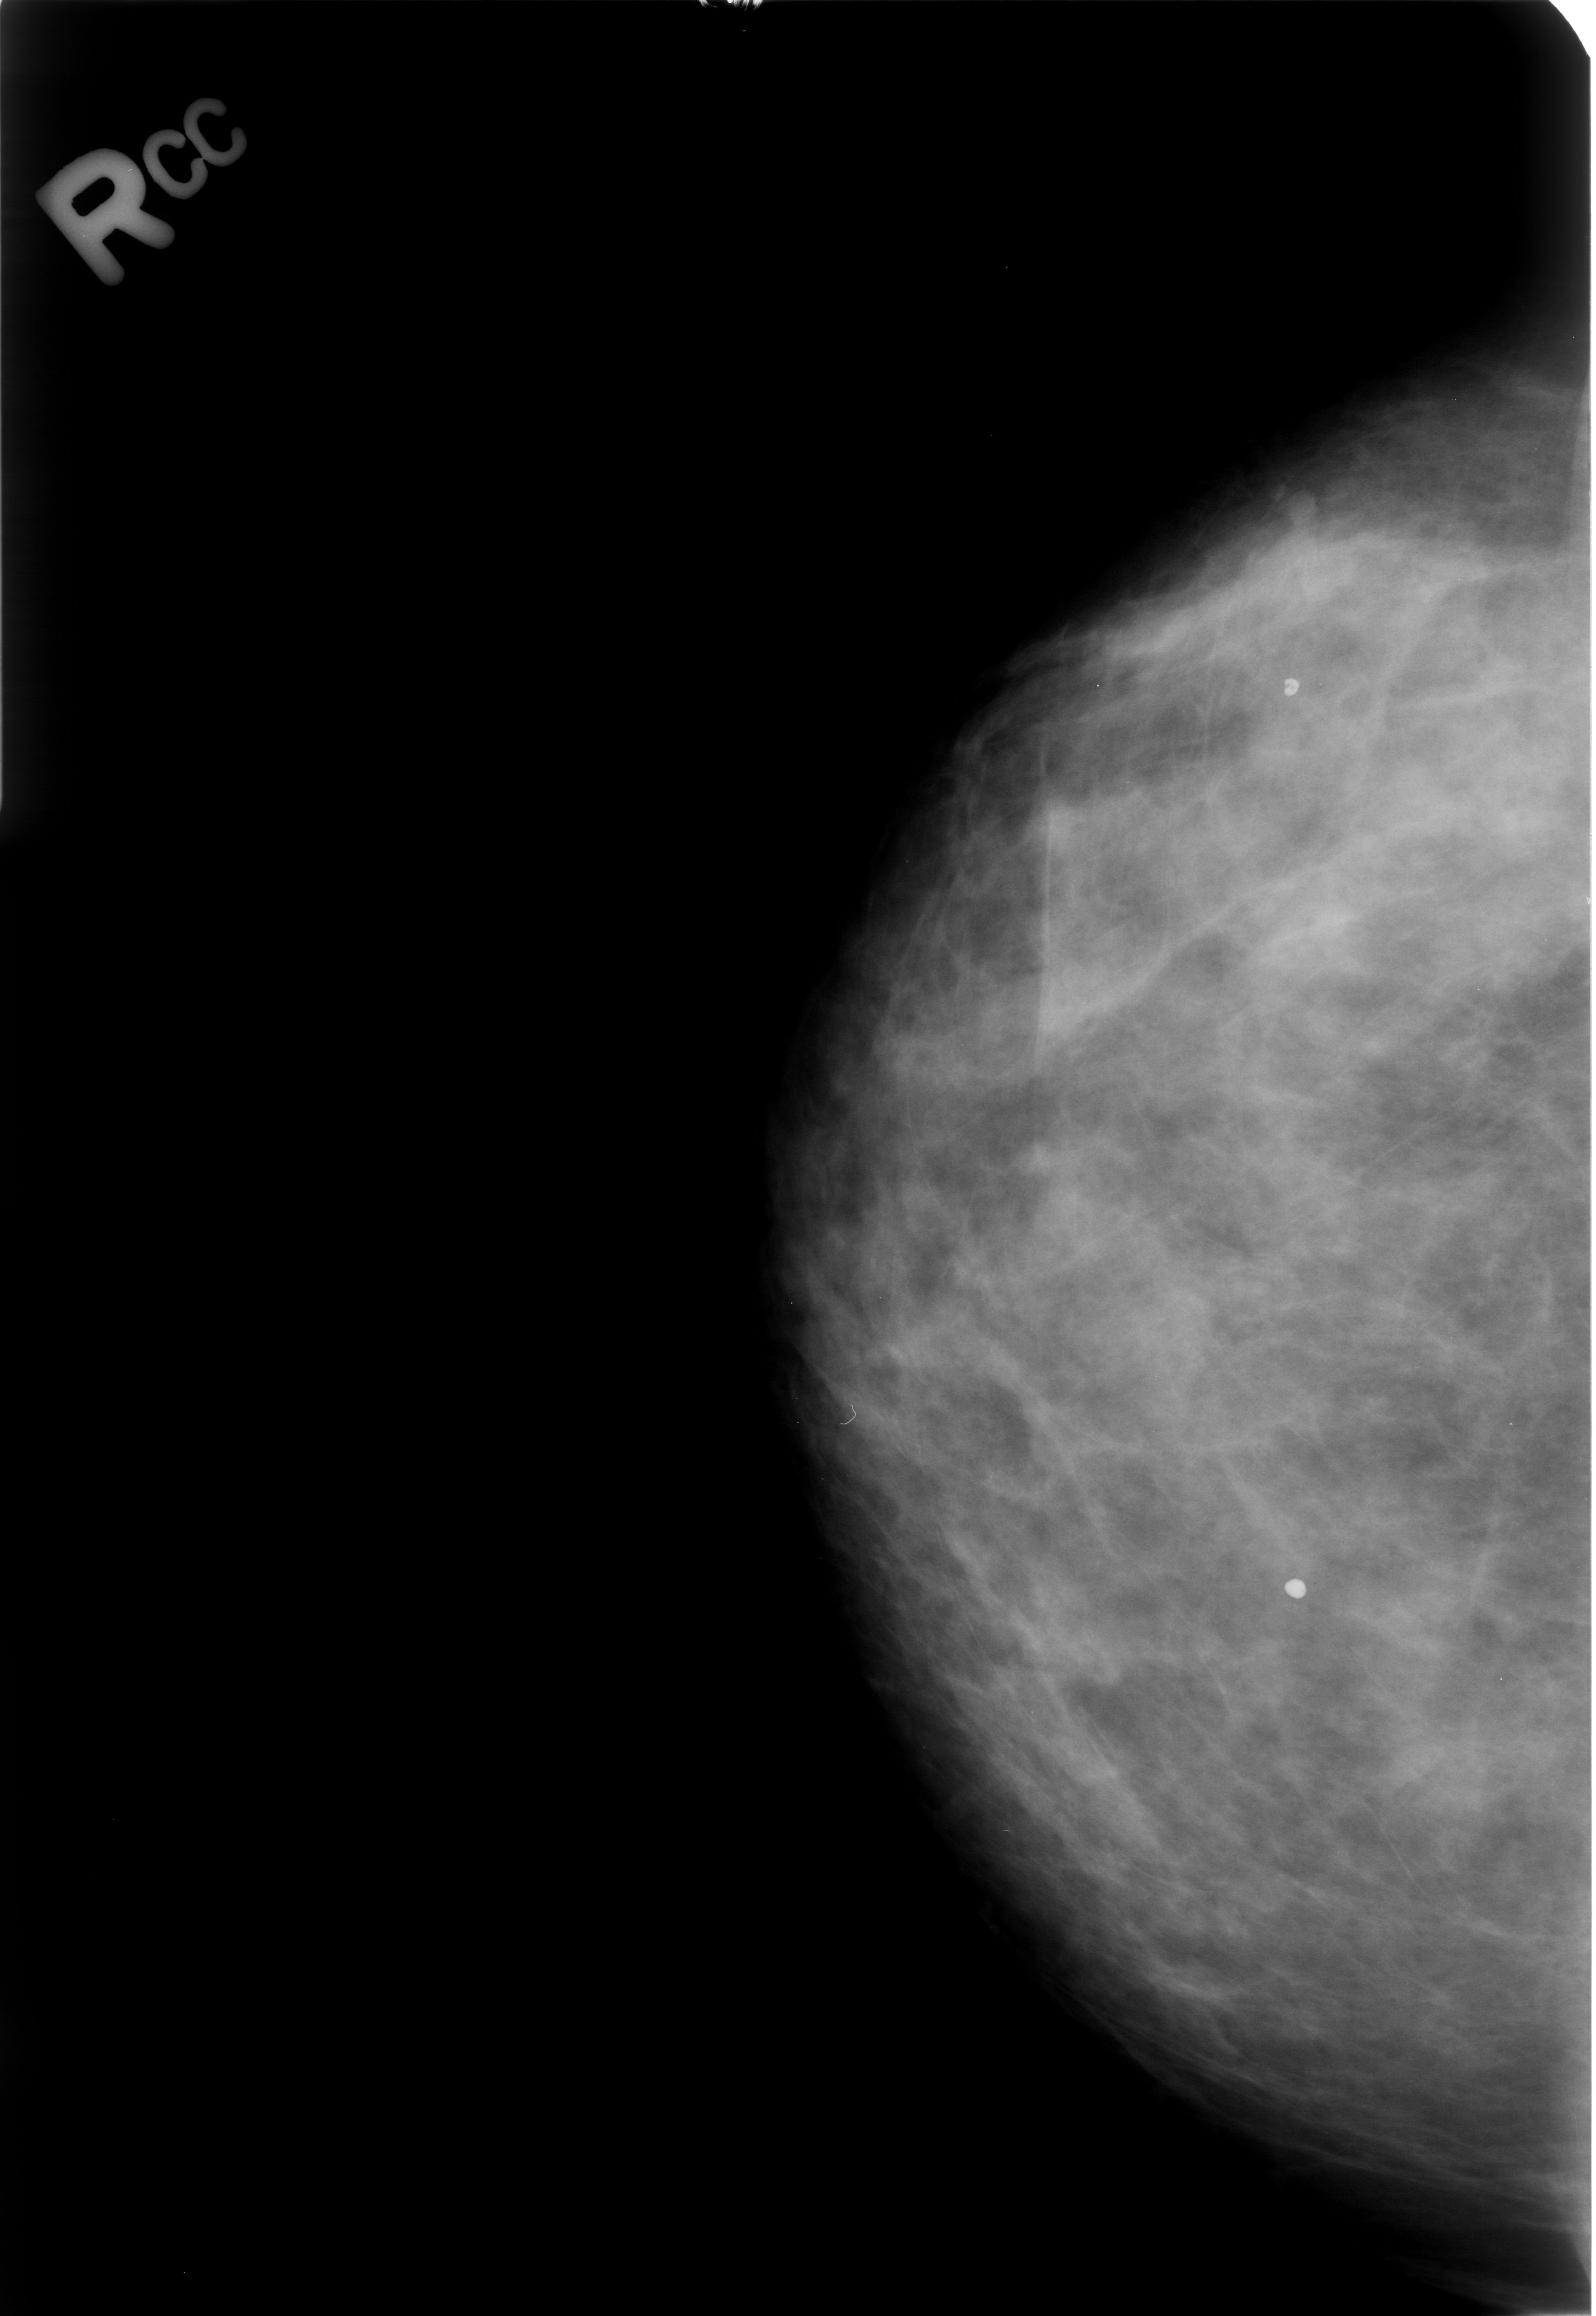
Digitized screen-film mammogram. Right breast. Craniocaudal (CC) view. Breast composition: heterogeneously dense (BI-RADS density category 3 of 4). 1596 × 2316 image matrix.
Marked abnormalities (boxes around the expert regions of interest):
- Finding 1 of 2: calcifications, morphology coarse / round and regular / lucent centered; BI-RADS assessment category 2; outcome (as recorded, no biopsy): benign without callback (not worked up further): bounding box [x1, y1, x2, y2] px = [1266, 666, 1317, 717]
- Finding 2 of 2: calcifications, morphology coarse / round and regular / lucent centered; BI-RADS assessment category 2; benign; no additional work-up was recommended (outcome (as recorded, no biopsy): benign without callback): [1271, 1563, 1330, 1614]